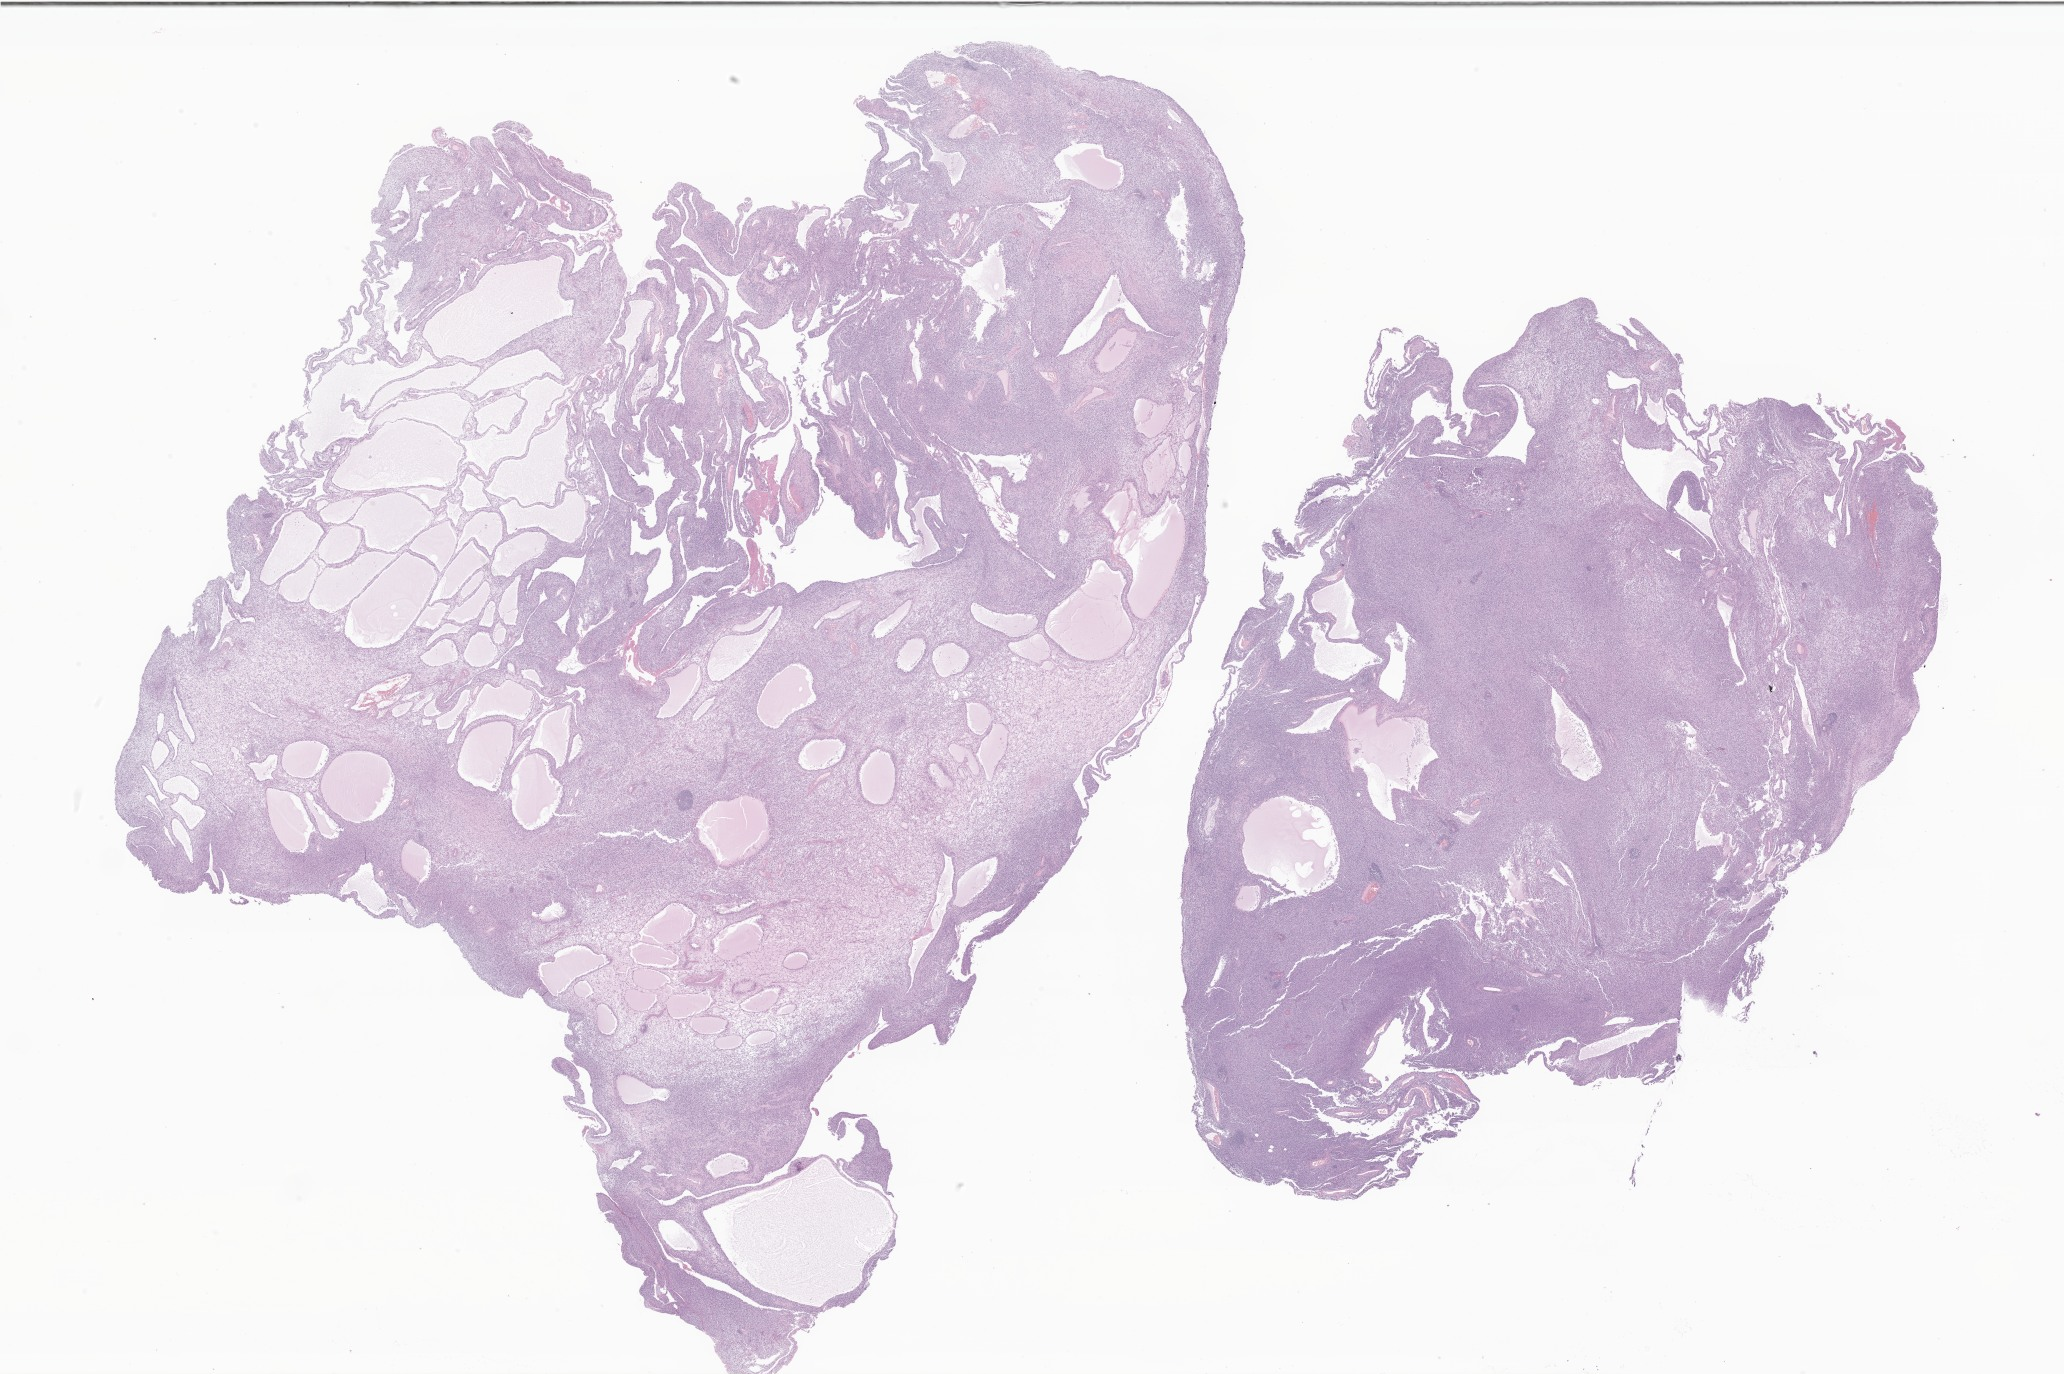
Whole-slide image, haematoxylin and eosin stain of tumor tissue from the soft tissue of lower extremity, shown as a low-resolution overview of the whole scanned area (about 34.8 x 23.2 mm); formalin-fixed, paraffin-embedded (FFPE) tissue. Patient: female, age 155 months (12 years 11 months).
Recorded diagnosis: Sarcoma, NOS.